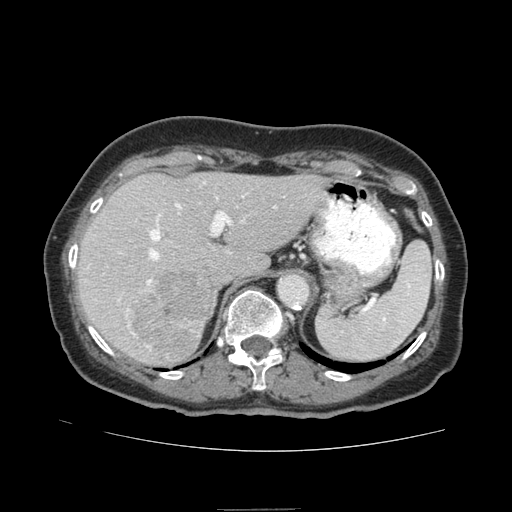
Contrast-enhanced abdominal CT (liver protocol), one axial slice; slice 55 of 95 in the series (ordered by position); reconstruction kernel STANDARD; soft-tissue window (W 400 / L 40 HU); 2.5 mm slice thickness; 512 × 512 image matrix, field of view 360 × 360 mm. Case-level facts recorded for this patient, not image findings: diagnosis: hepatocellular carcinoma (patient treated with transarterial chemoembolisation; whether this scan precedes or follows treatment is not stated here); TNM stage (as recorded): Stage-IVA; Child-Pugh class: B; tumour nodularity: uninodular.
Outlined on this slice (semi-automatic segmentation, software-assisted and operator-edited):
- liver parenchyma outside the tumour (the mass and vessels are separate outlines, so this box may not span the whole liver): box from (x=76, y=172) to (x=327, y=366) px
- mass: (x=126, y=271)–(x=215, y=358)
- liver vessels: (x=118, y=182)–(x=276, y=347)